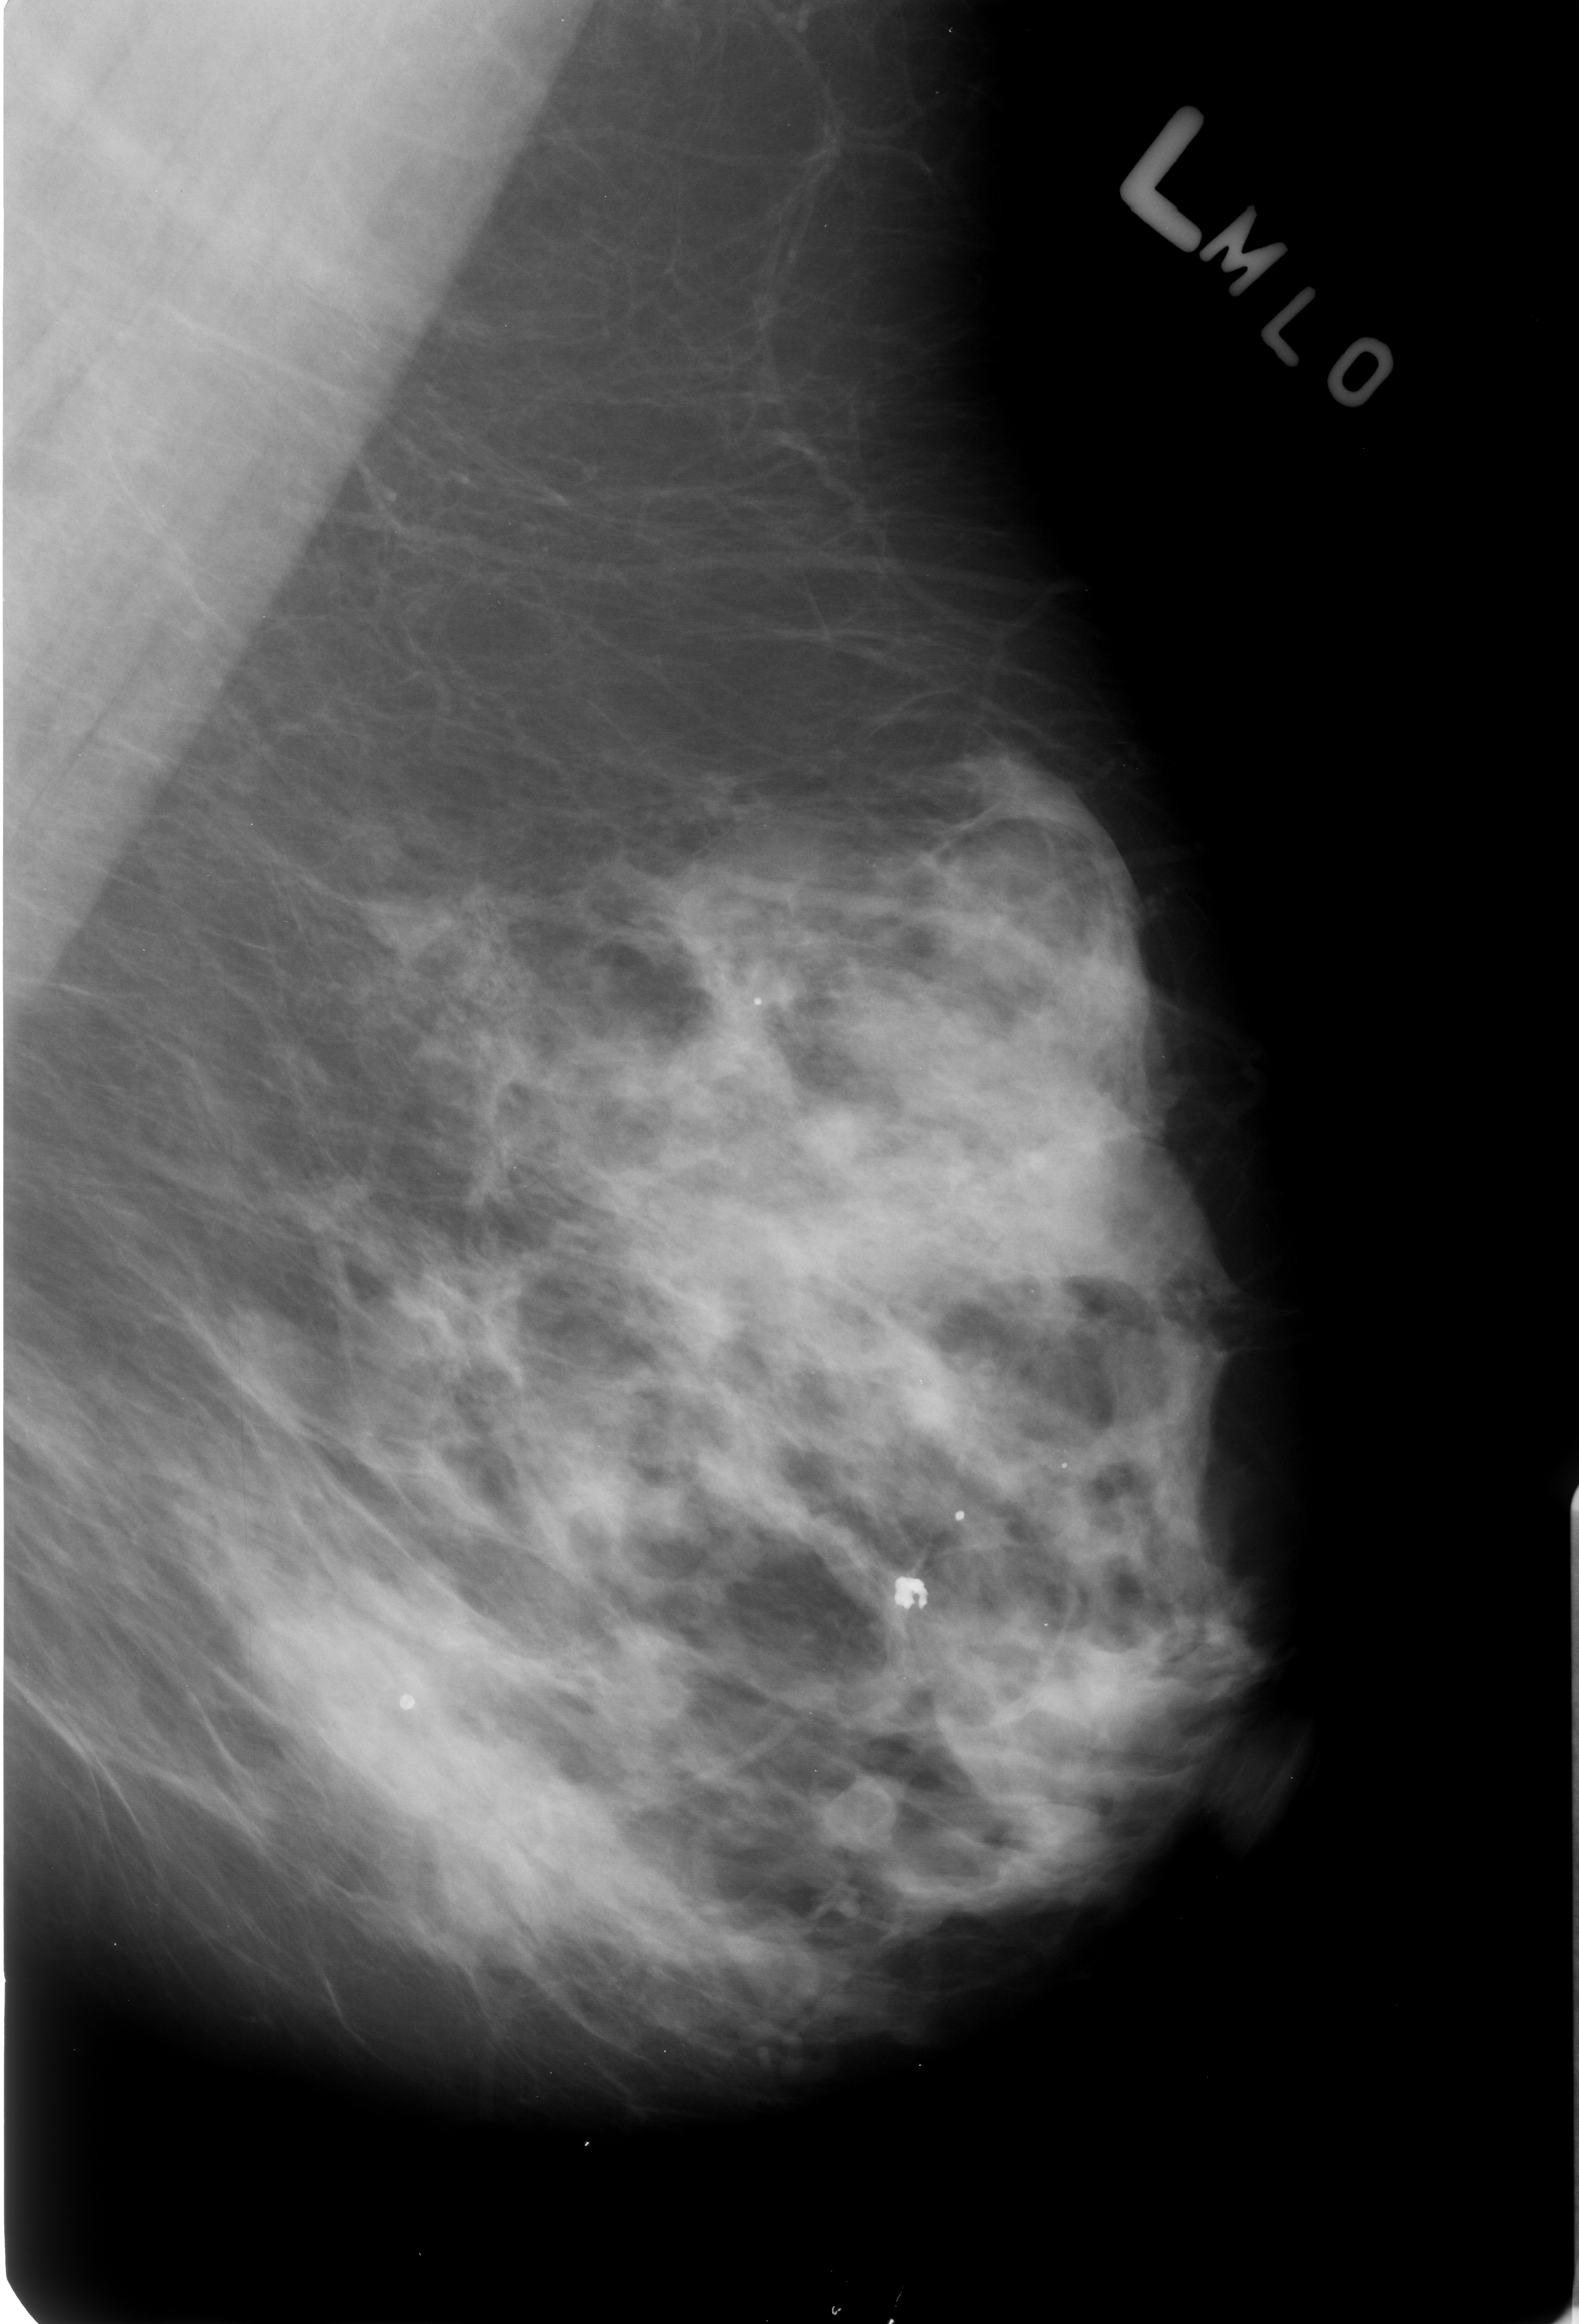
Digitized screen-film mammogram; left breast; MLO view; BI-RADS breast density category 3 (scale 1–4).
Calcifications, morphology round and regular / lucent center / dystrophic, distribution diffusely scattered; BI-RADS assessment category 2; benign; no additional work-up was recommended (benign without callback).